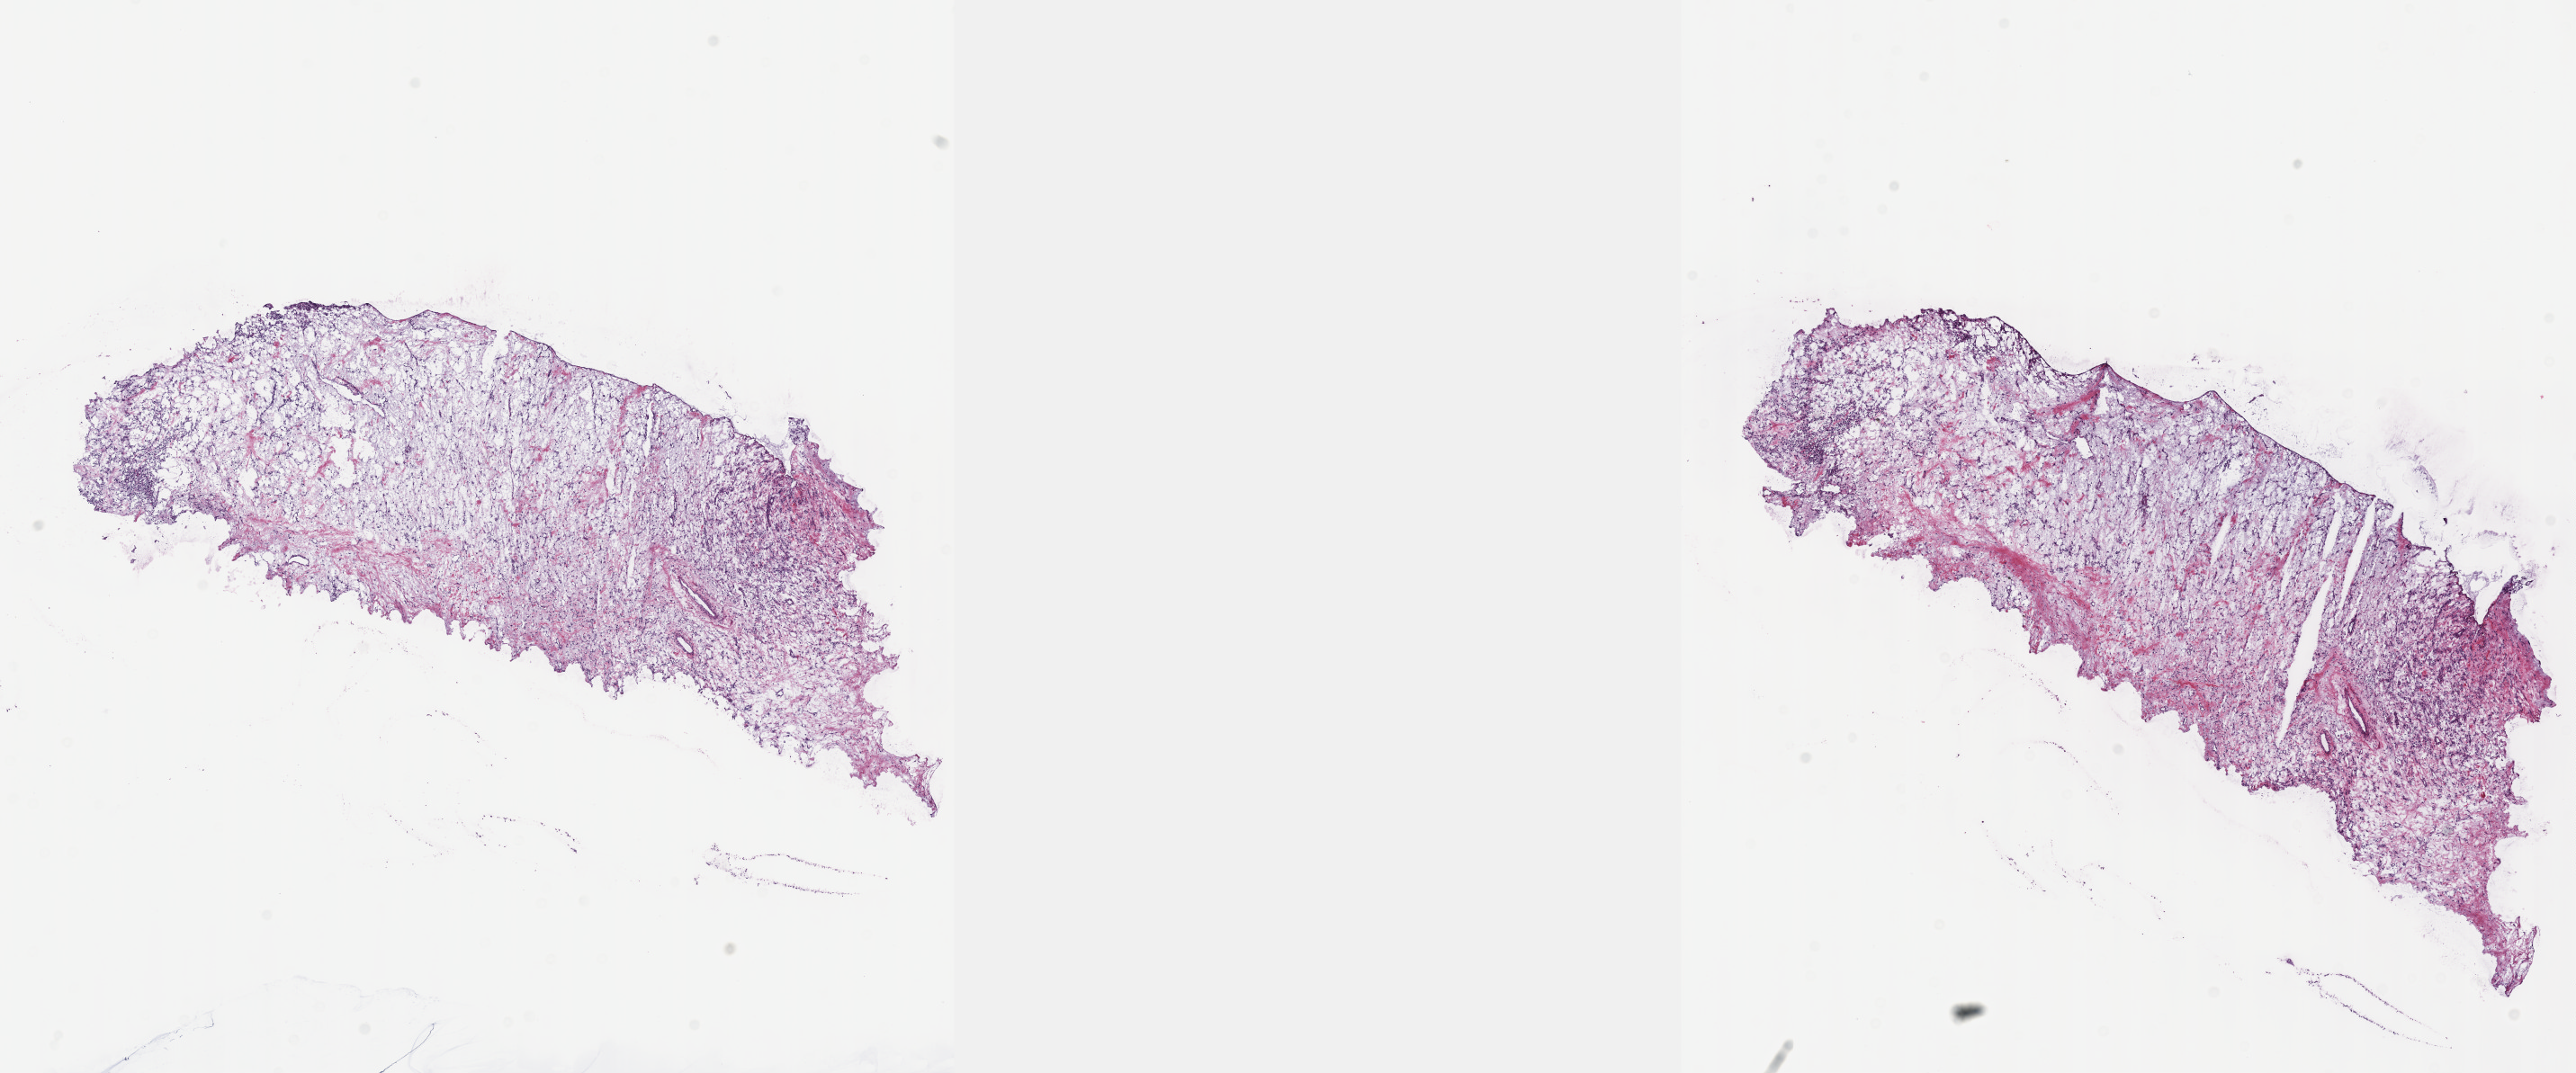
Digitized H&E tissue section (whole slide), shown as a low-resolution overview of the whole scanned area (about 23.1 x 9.6 mm); frozen section from the top of the tissue portion; sample: primary tumour, kidney. Female patient; age at initial diagnosis 60 years. Histologic grade: G2 (moderately differentiated). Pathologist review of this section (percent, as recorded): tumour cells 80%, tumour nuclei 80%, normal cells 0%, stromal cells 20%, necrosis 0%. Inflammatory infiltration, as recorded: lymphocyte infiltration 2%, monocyte infiltration 1%, neutrophil infiltration 1%.
AJCC pathologic stage: I (7th edition). TNM: T1b NX. Histologic diagnosis: Clear cell adenocarcinoma, NOS.